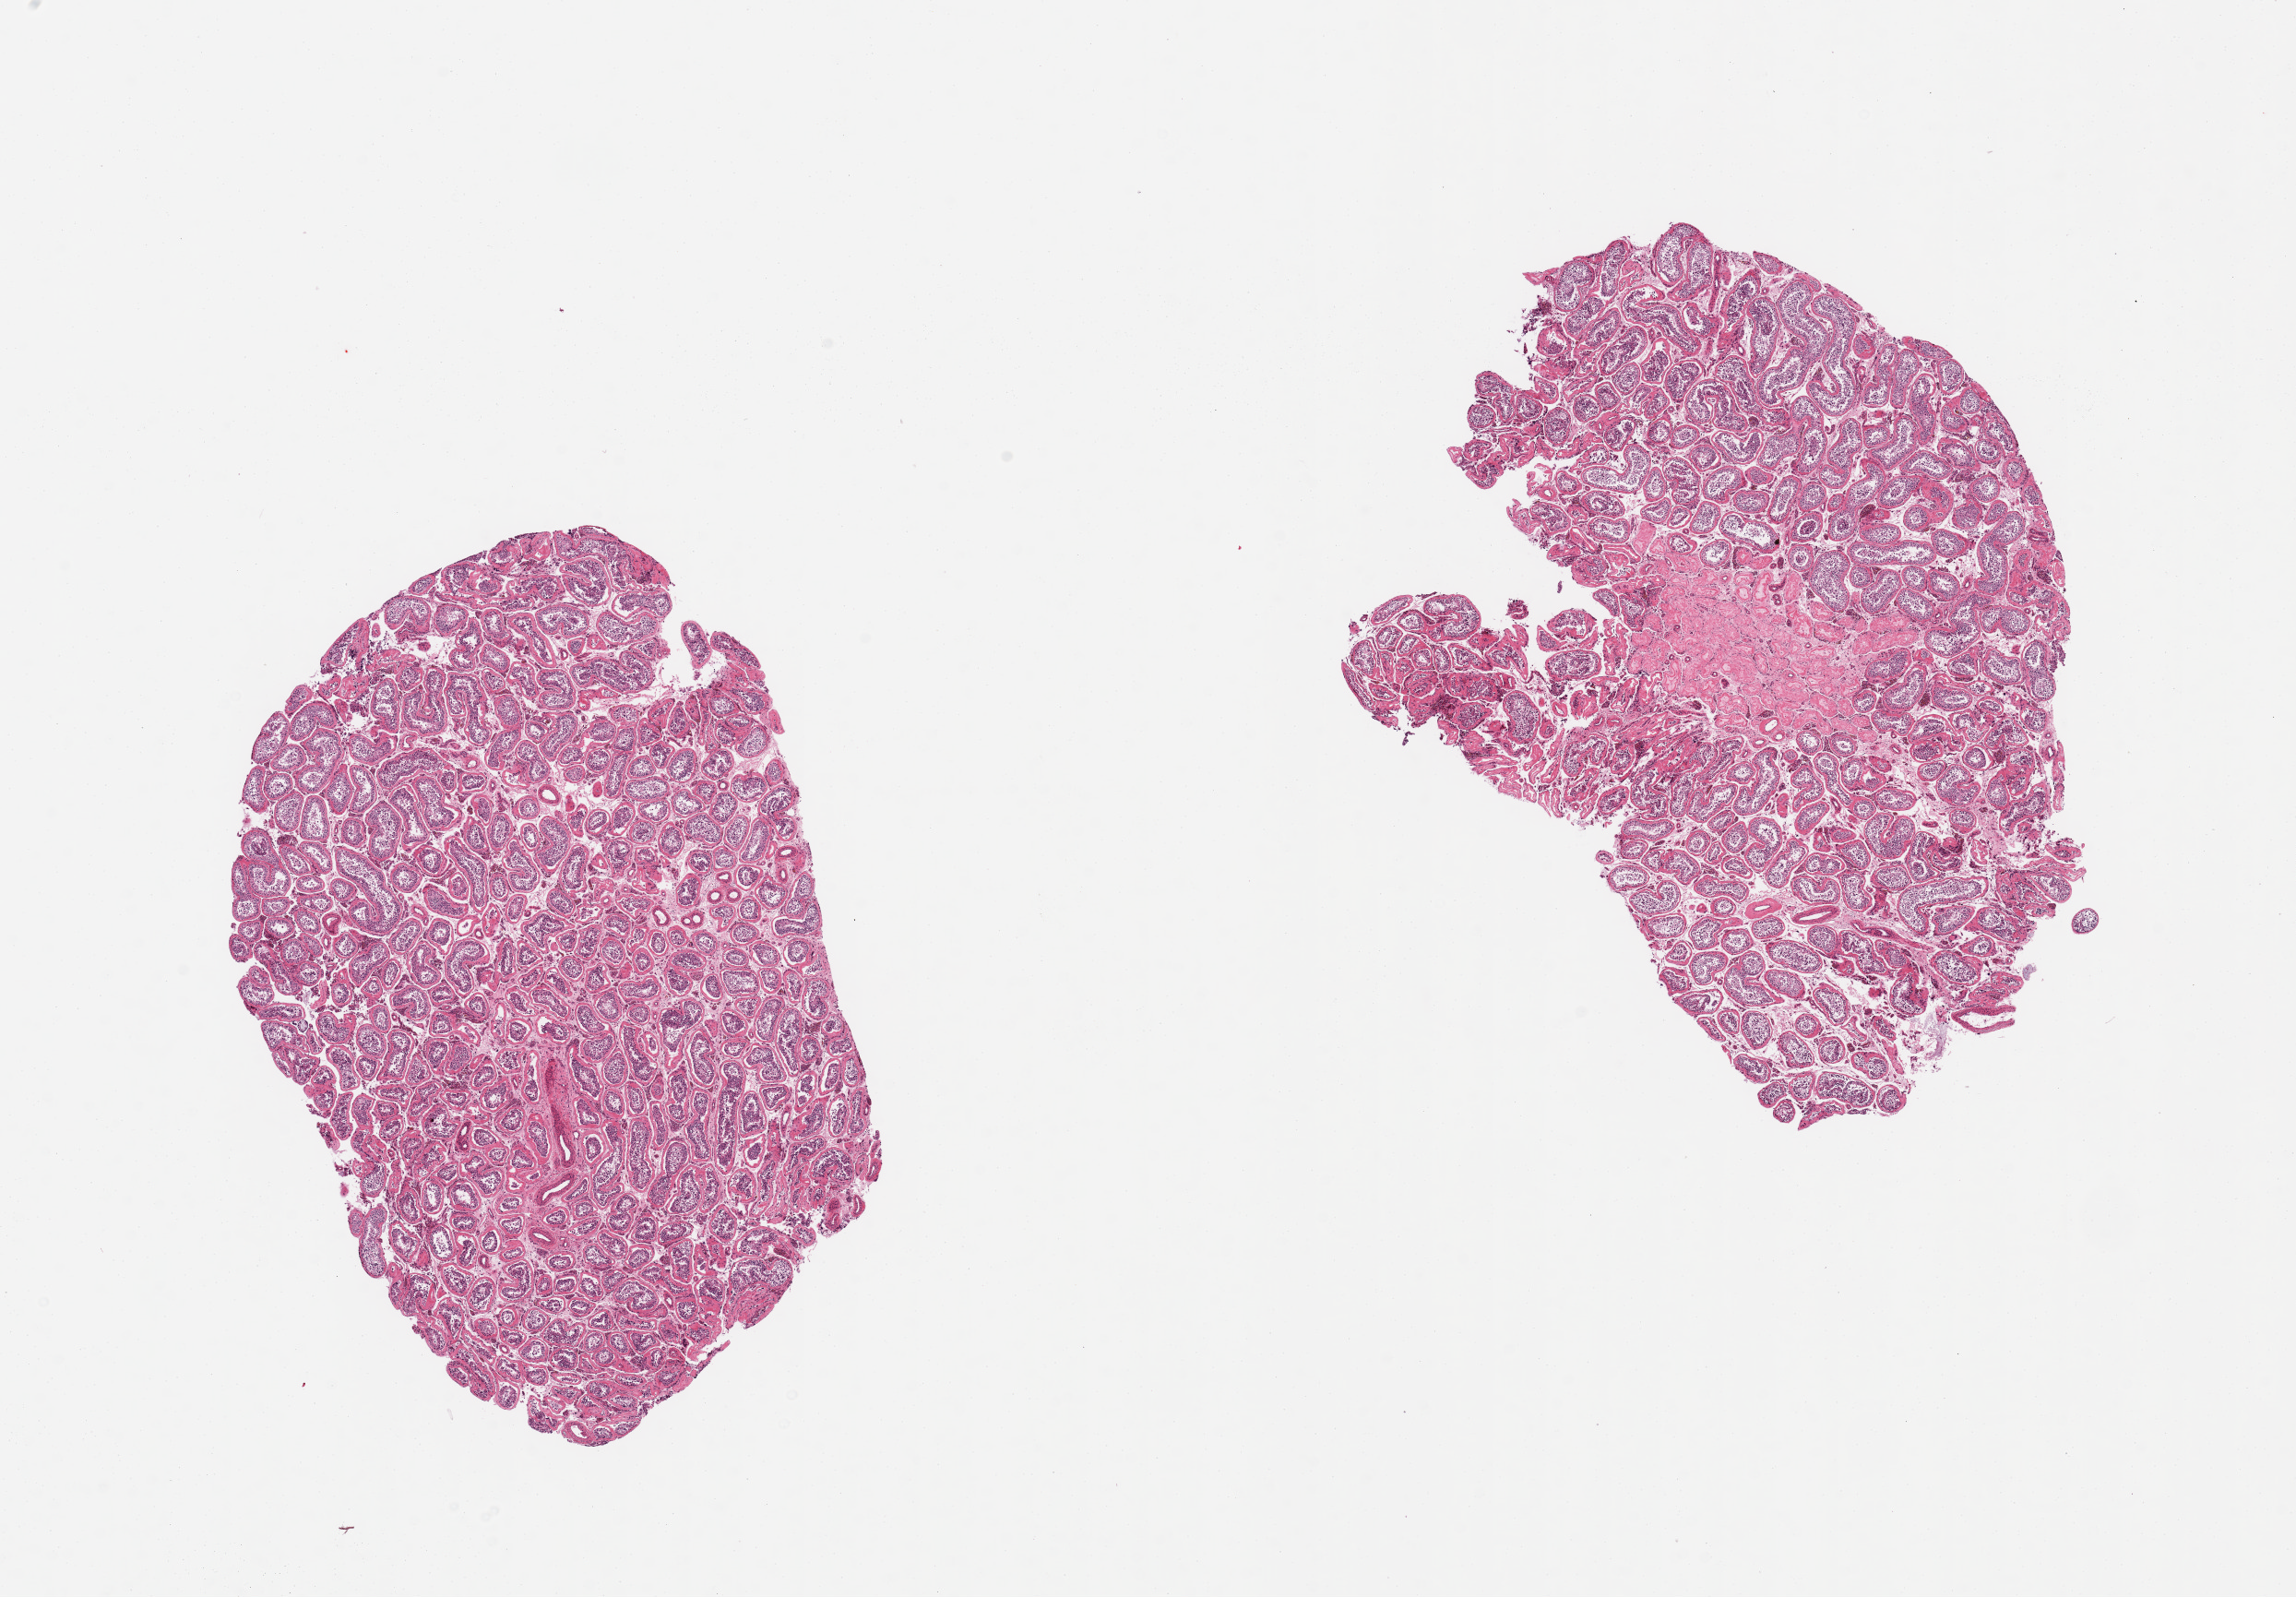
Whole-slide image, hematoxylin and eosin (H&E) stain, brightfield, shown as a low-resolution overview of the whole scanned area (about 19.7 x 13.7 mm, acquisition: 20x scan); PAXgene-fixed paraffin-embedded (PFPE) section; sampled site (target tissue): testis; donor tissue sample. Donor: male.
Pathologist's review note for this sample: 2 pieces, spermatogenesis is present.